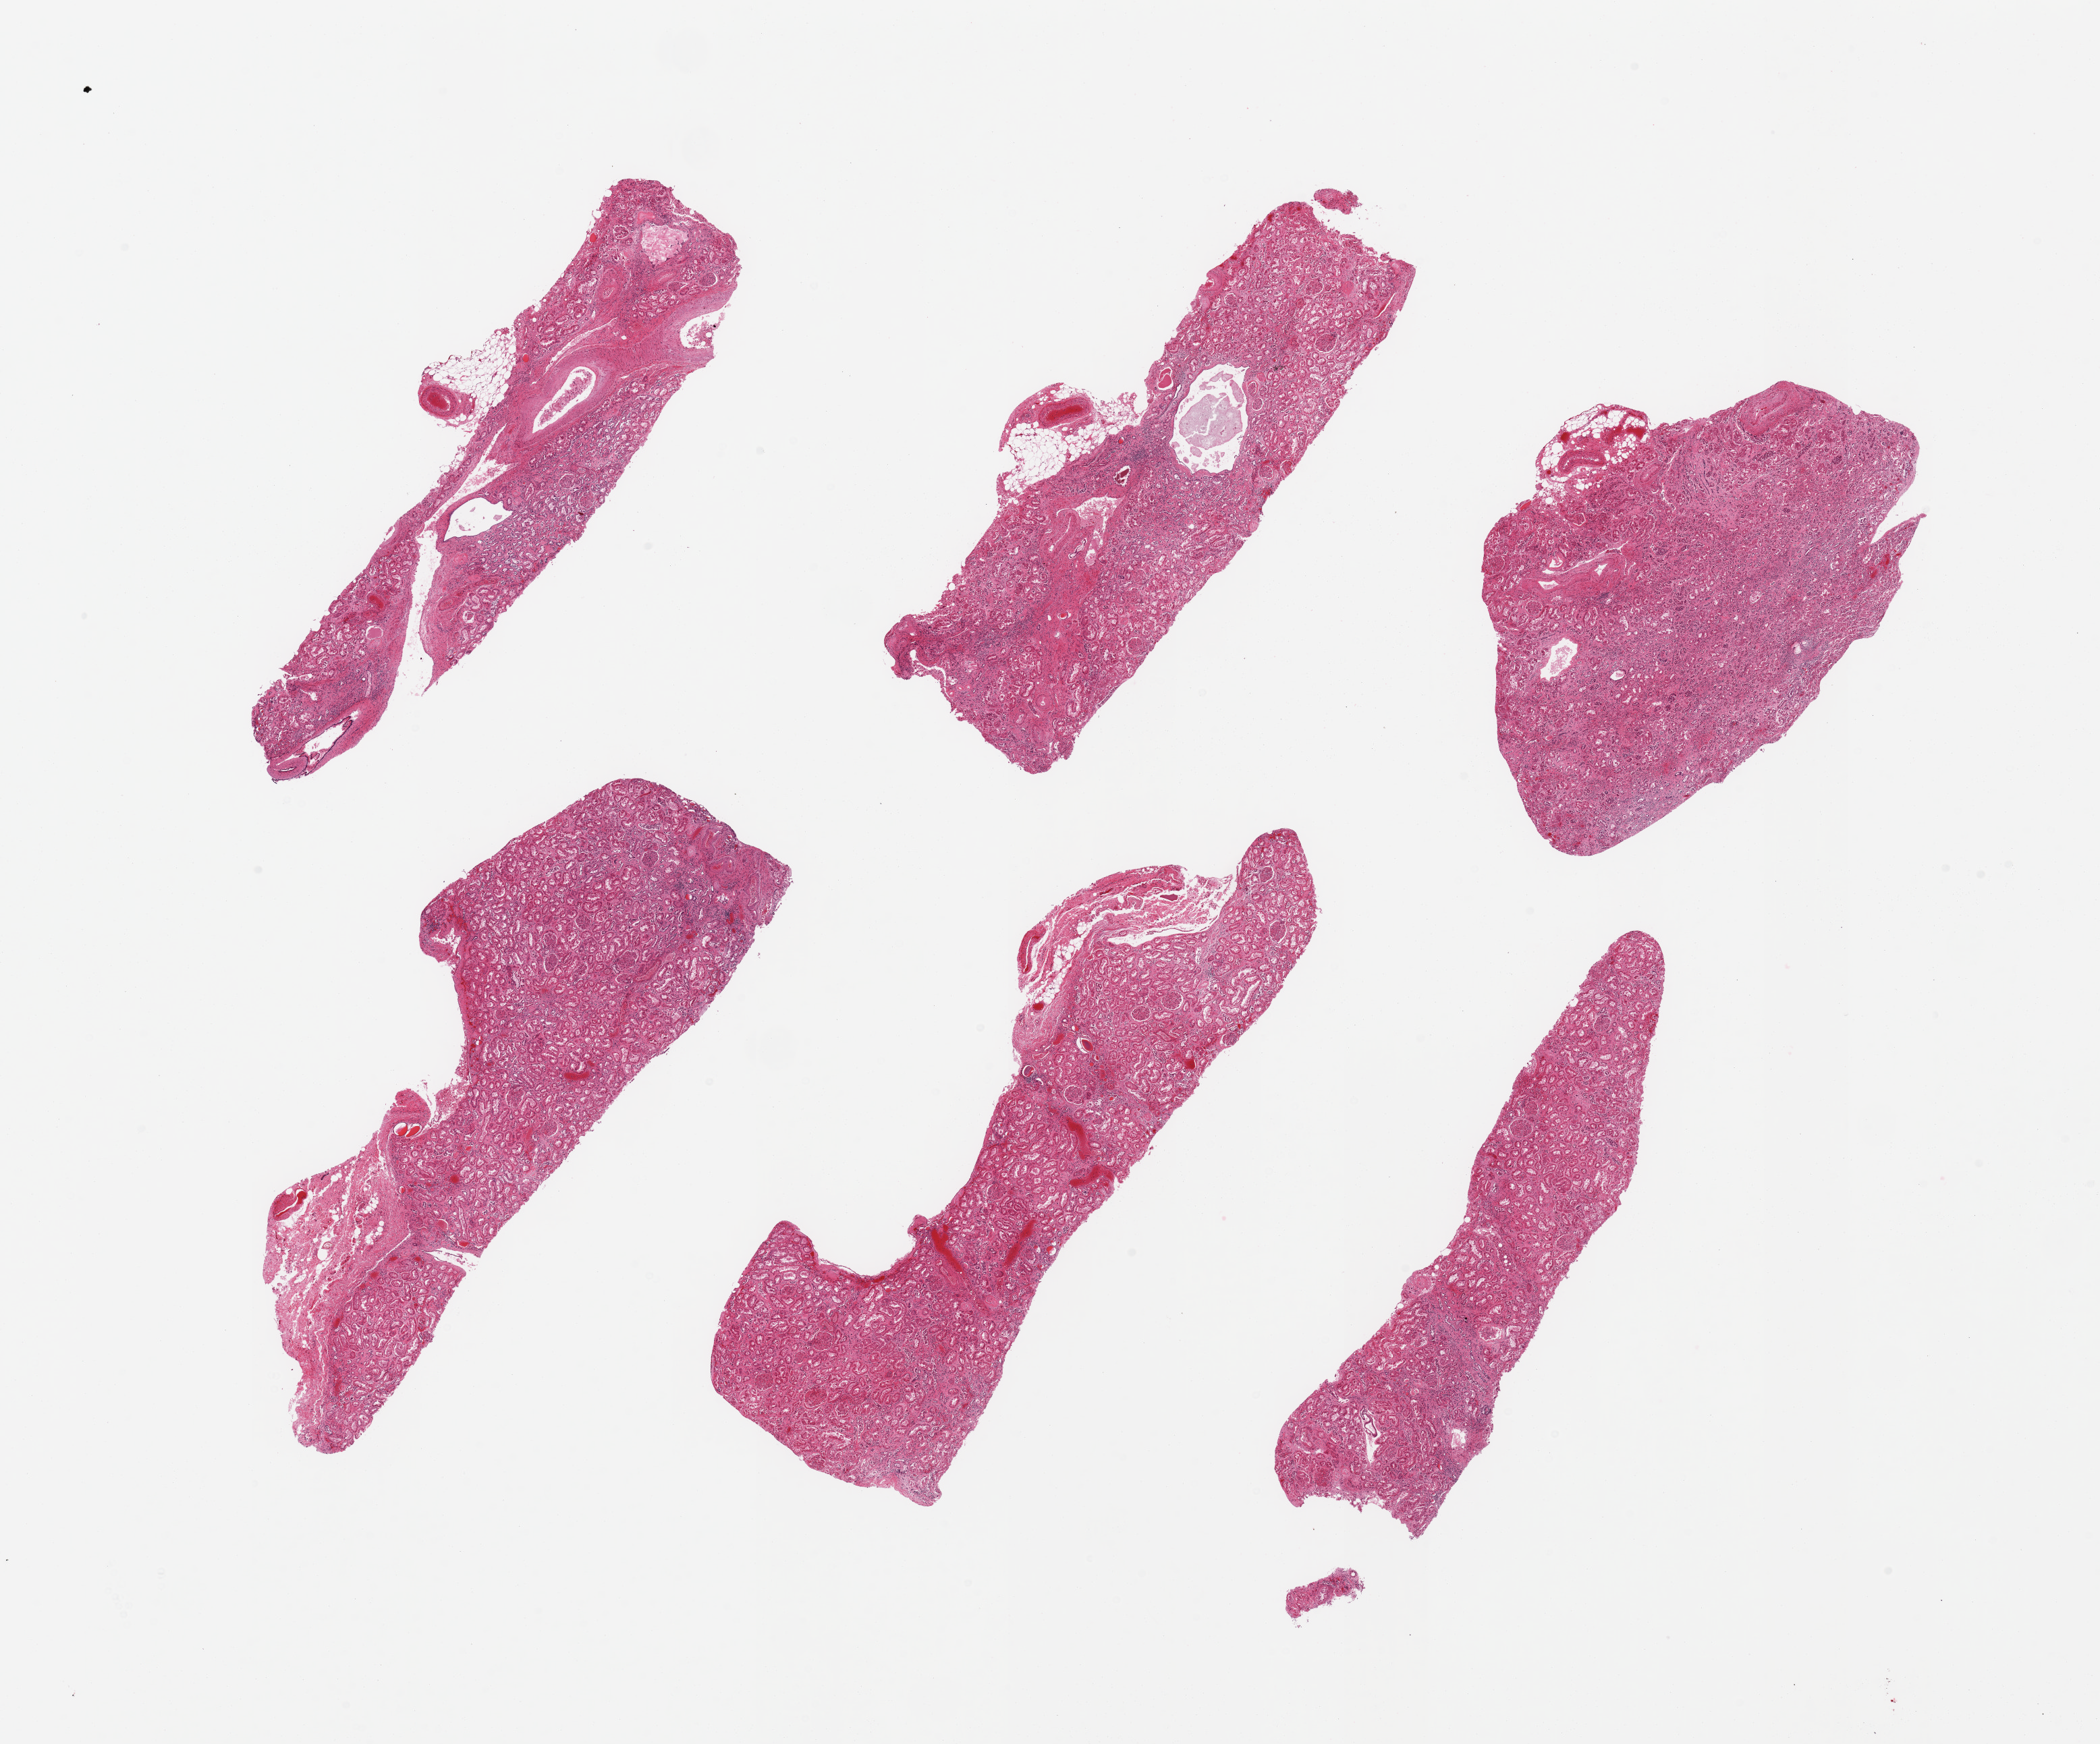
Haematoxylin and eosin whole-slide image, shown as a low-resolution overview of the whole scanned area (about 24.6 x 20.4 mm), PAXgene-fixed, paraffin-embedded tissue, target tissue: renal cortex, donor tissue sample. Donor: female.
Reviewer comment on this tissue sample: 6 pieces, glomeruli present, tubules with advanced autolysis. Prominent glomerulo-sclerosis, interstitial fibrosis.